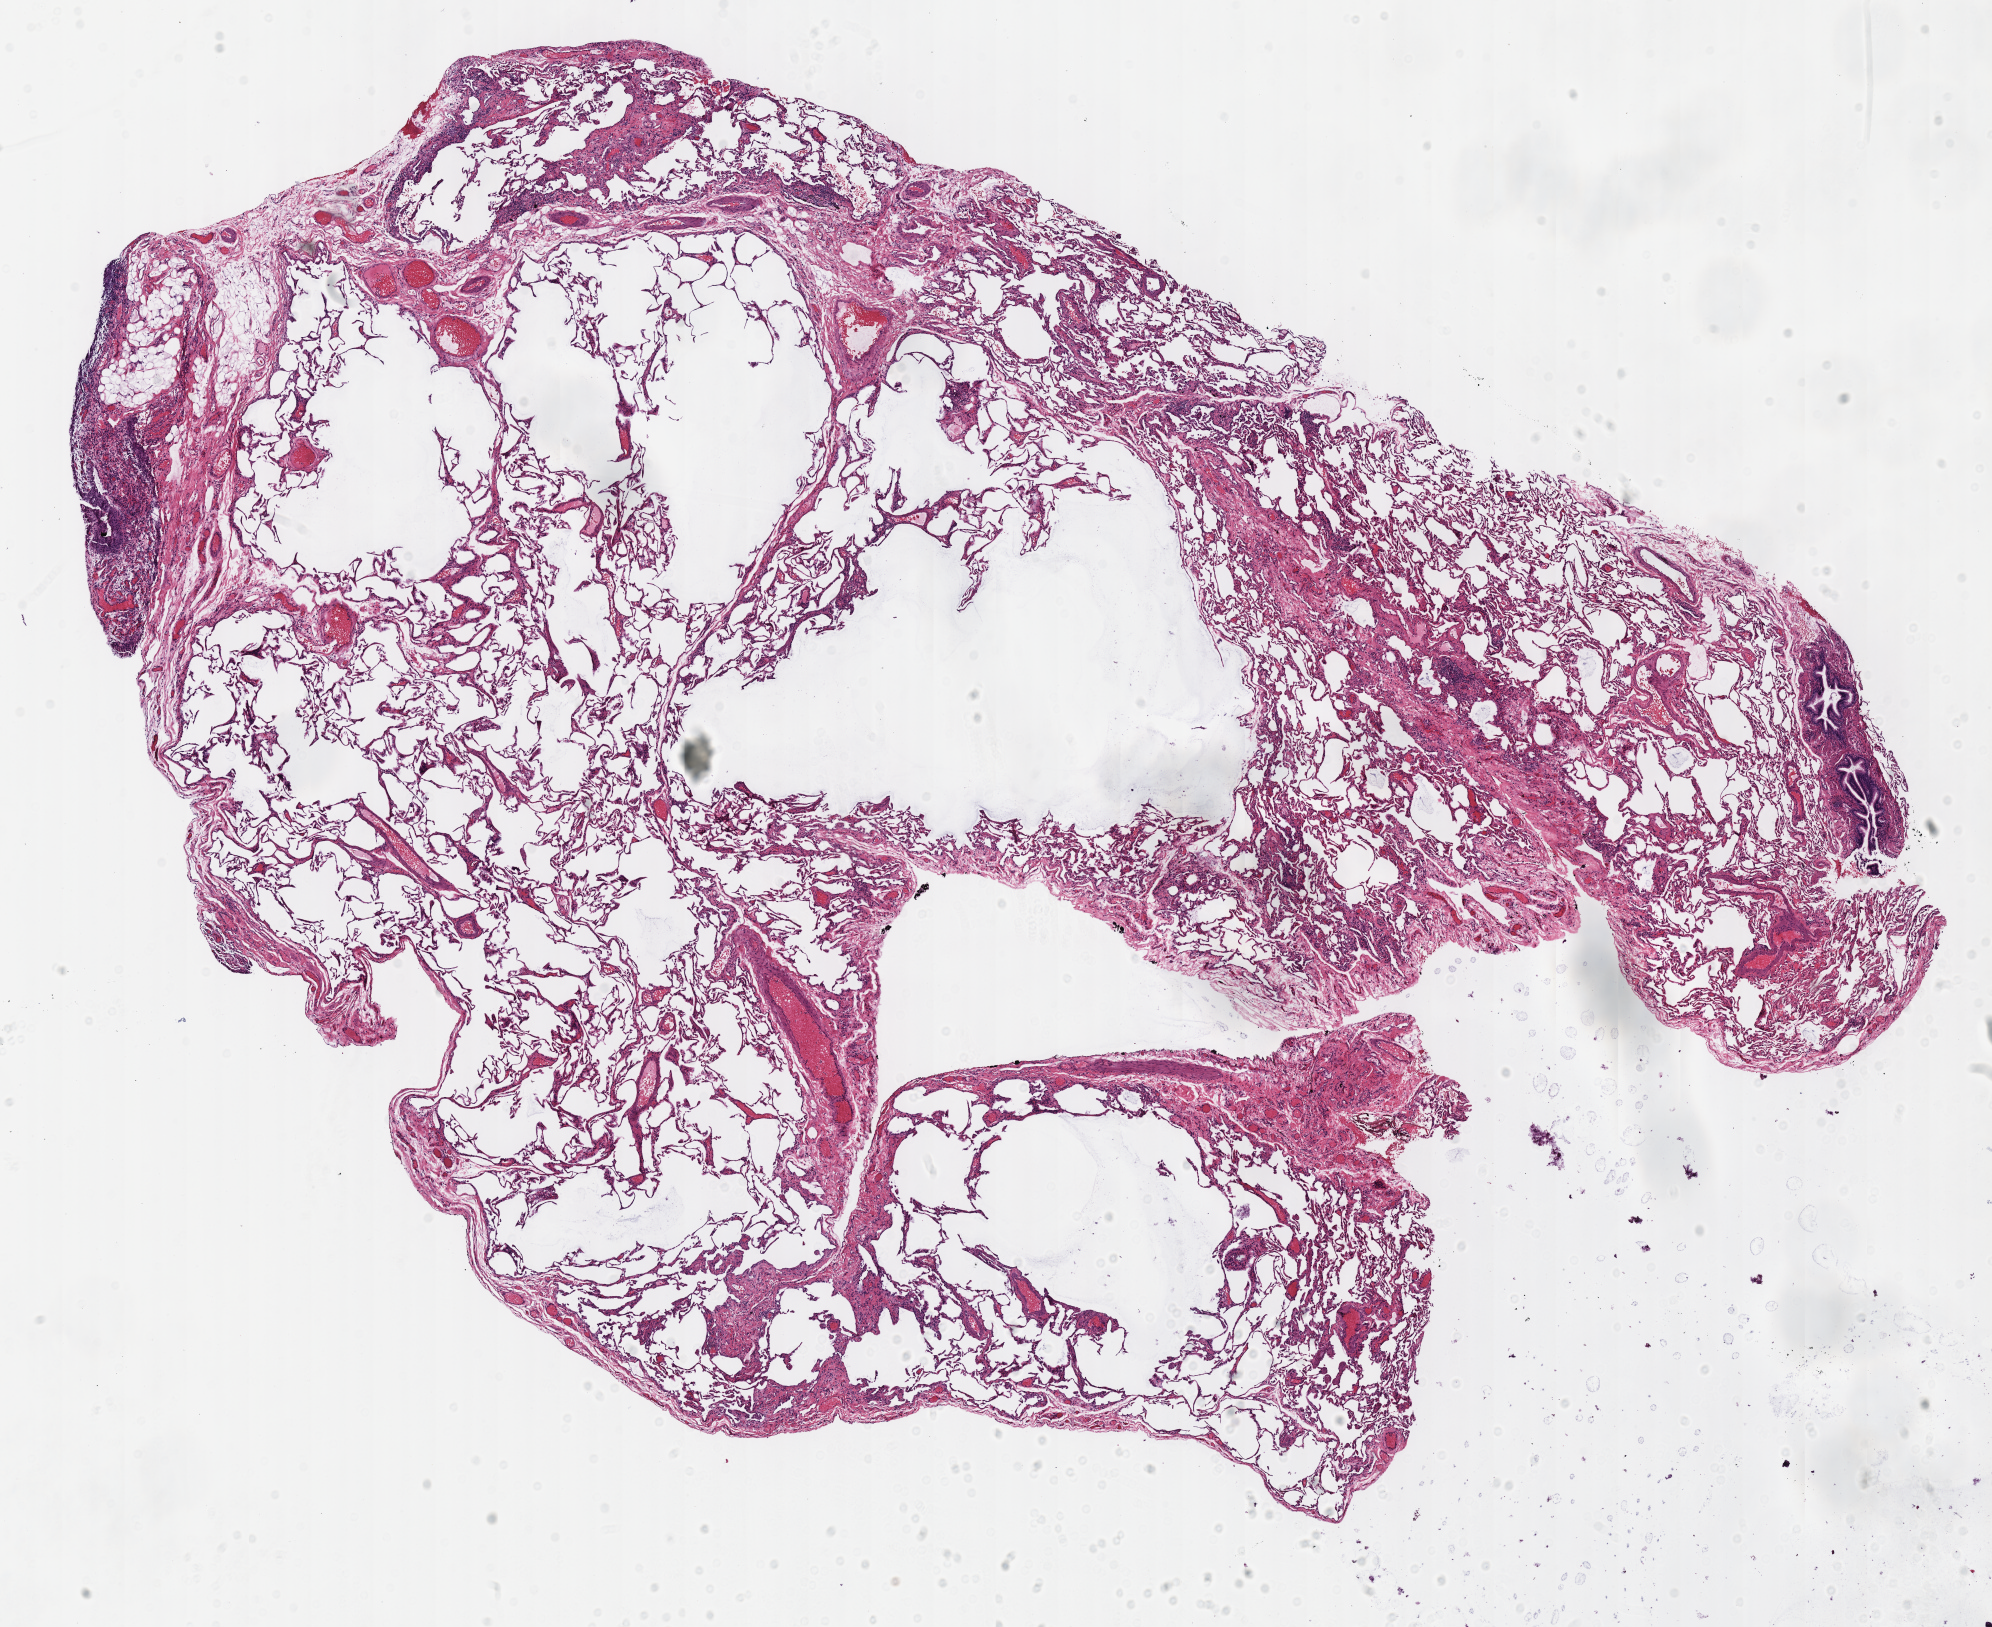
Digitized Hematoxylin and eosin (H&E) stained tissue section (whole slide), a low-resolution overview of the entire scanned area, about 15.7 x 12.8 mm; frozen section; sample: solid tissue normal (non-tumour tissue), lung. Patient: female, age at initial diagnosis 69 years.
This section: solid tissue normal sample (biorepository sample class). Patient diagnosis: Adenocarcinoma, NOS (lower lobe, lung).